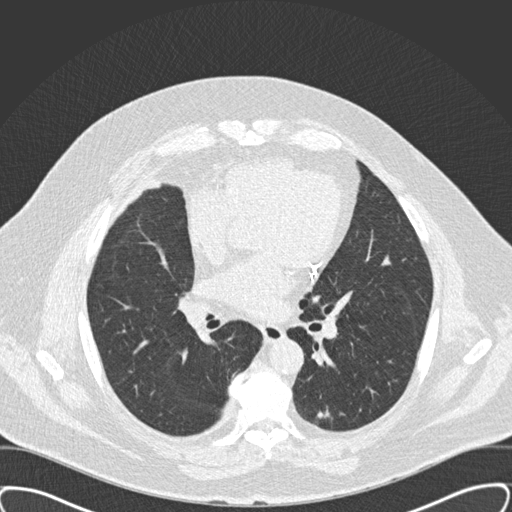
Low-dose screening chest CT, one axial slice. Position 89 of 159 along the scan axis. Reconstruction kernel B30f. 120 kVp. Lung window (W 1500 / L -600 HU). 2 mm slice thickness. 512 × 512 image matrix, field of view 400 × 400 mm.
Outlined on this slice (expert manual segmentation):
- lesion 1 (tumor, lower lobe of left lung): bounding box [x1, y1, x2, y2] px = [318, 410, 329, 418]